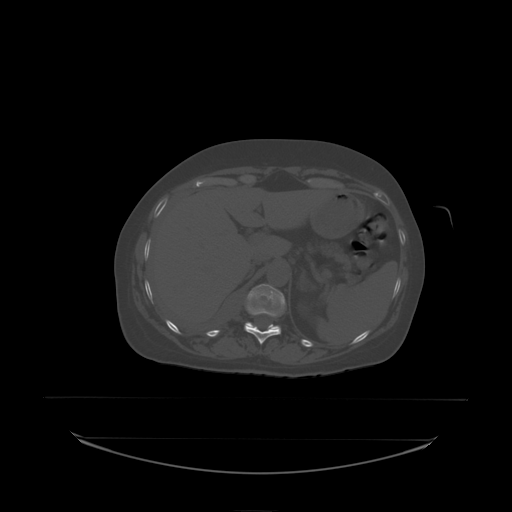
CT including the spine, one axial slice; slice 101 of 242 in the series (ordered by position); bone window (W 1800 / L 400 HU); 2.5 mm slice thickness; 512 × 512 image matrix. Patient: female, 53 years. Case-level facts recorded for this patient, not image findings: primary cancer: lung; vertebrae with lytic lesions (as recorded): T7, L1.
Outlined on this slice (semi-automatic segmentation, software-assisted and operator-edited):
- T11 vertebra: bounding box [x1, y1, x2, y2] px = [245, 306, 281, 338]
- T12 vertebra: [246, 284, 286, 330]